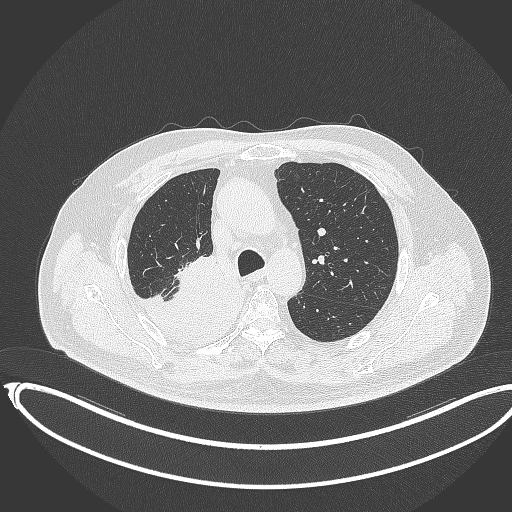
Chest CT, one axial slice. Slice 252 of 403 in the series (ordered by position). 120 kVp. Lung window (W 1500 / L -600 HU). 1 mm slice thickness. 512 × 512 image matrix, field of view 436 × 436 mm. Patient: male, 68 years. Case-level facts recorded for this patient, not image findings: clinical TNM (as recorded): T2a N0 M0.
Outlined on this slice (rectangle marked by the reading radiologist):
- lung tumour (recorded histology: adenocarcinoma): bounding box <131,256,241,348> (left, top, right, bottom; pixels)